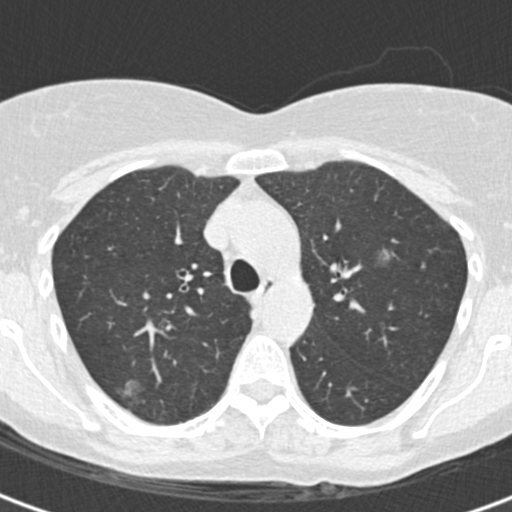
Low-dose screening chest CT, one axial slice. Slice 125 of 172 in the series (ordered by position). Lung window (W 1500 / L -600 HU). 512 × 512 image matrix, field of view 283 × 283 mm.
Annotated regions visible in this slice (manually delineated by an expert):
- lesion 1 (tumor, upper lobe of right lung): bounding box <122,379,145,407> (left, top, right, bottom; pixels)